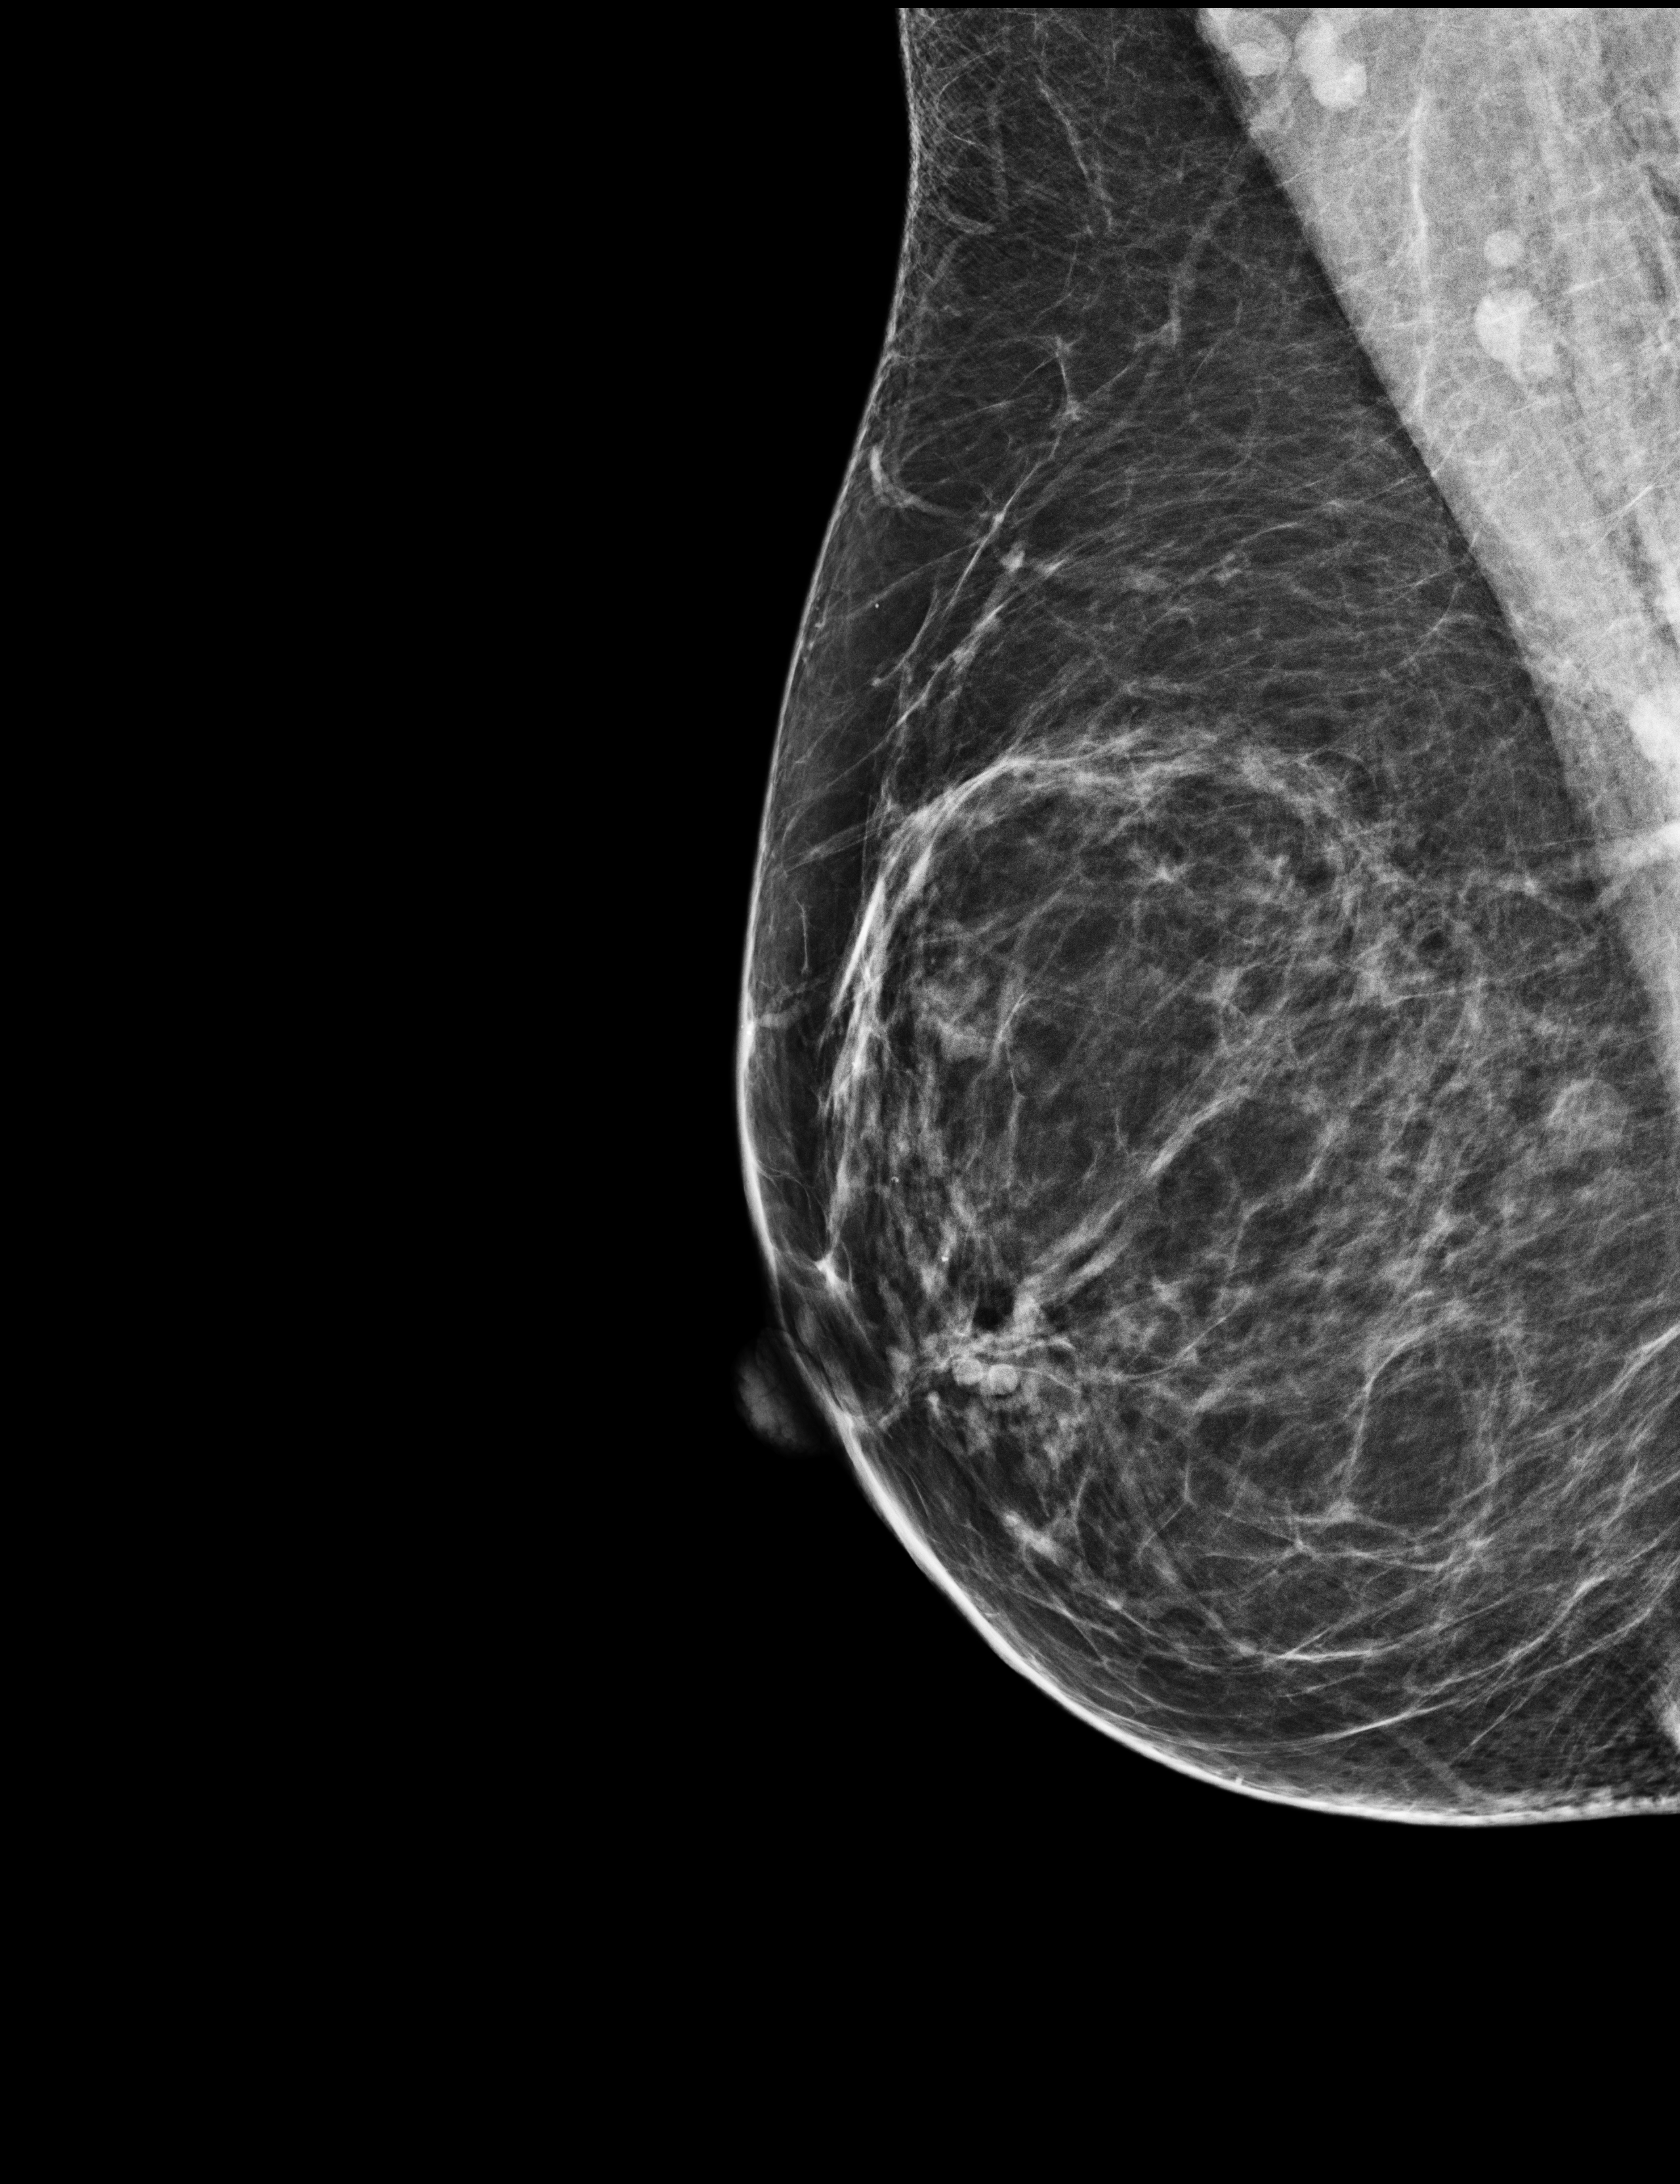
Annual screening mammography examination. Female patient, age 55 years.
Image type: full-field digital mammogram. Breast: right. Projection: mediolateral oblique (MLO) view.